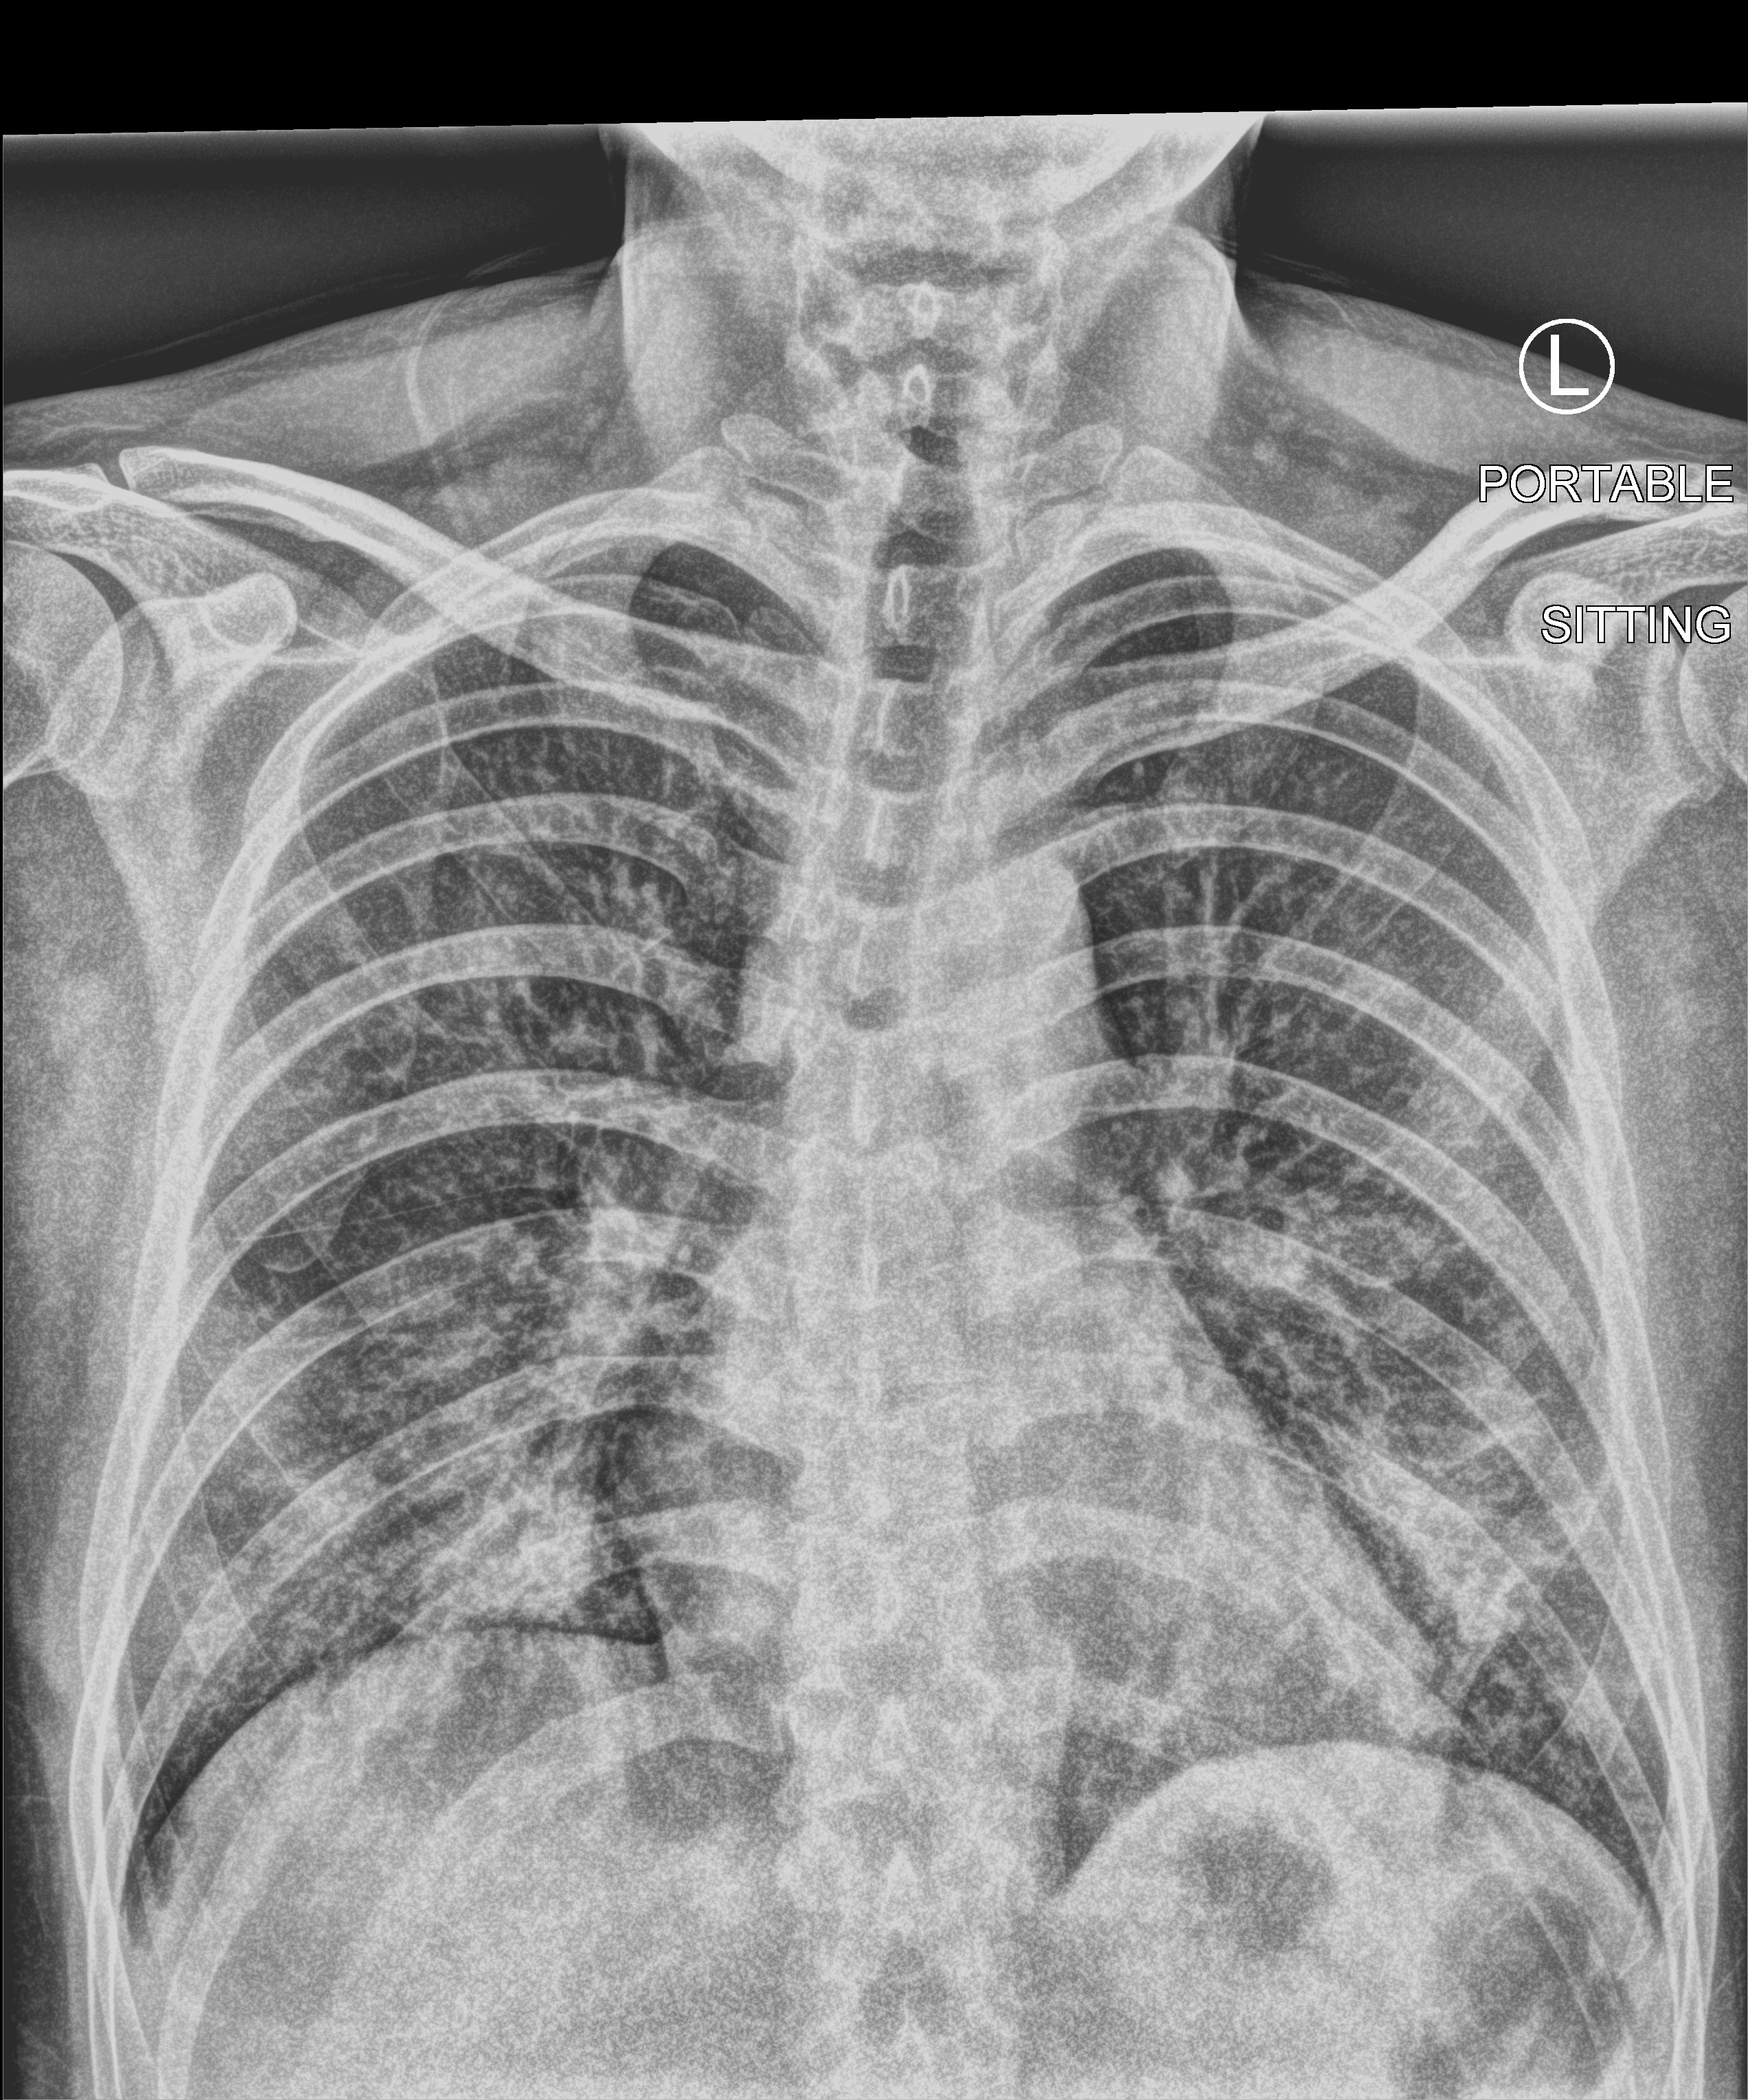
Portable chest radiograph, anteroposterior (AP) projection. Male patient hospitalised with COVID-19, age 18–59 years.
Admission-level facts for this patient (not findings on this image; timing relative to this image not recorded): admitted to intensive care during this hospital stay: no; length of hospital stay: 14 days.